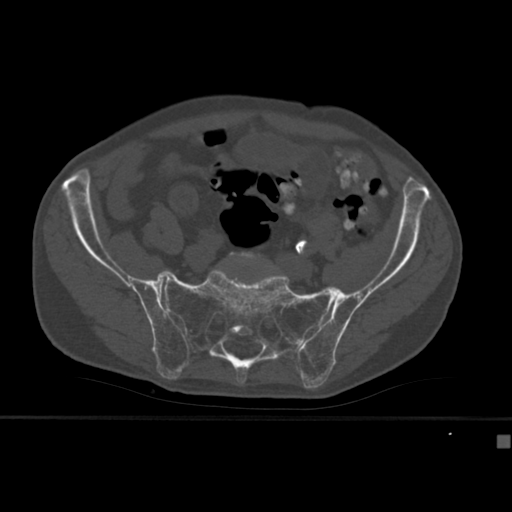
CT including the spine, one axial slice; slice 66 of 430 in the series (ordered by position); 120 kVp; bone window (W 1800 / L 400 HU); 1.5 mm slice thickness; 512 × 512 image matrix, field of view 337 × 337 mm. Patient: male, 64 years. From the clinical record (not read from this slice): primary cancer: uterus.
Annotated regions visible in this slice (semi-automatic segmentation, software-assisted and operator-edited):
- L5 vertebra: bounding box <229,252,275,270> (left, top, right, bottom; pixels)